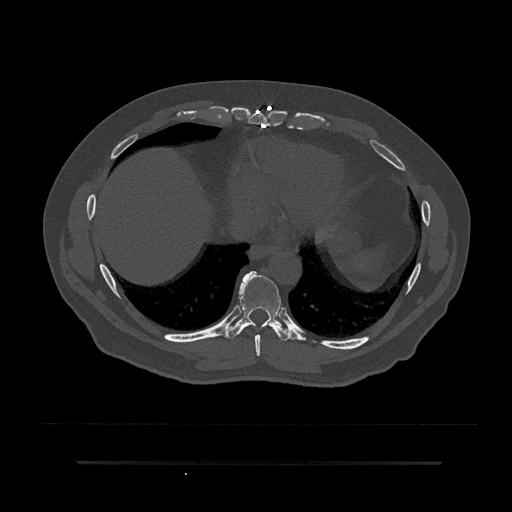
CT including the spine, one axial slice. Position 393 of 797 along the scan axis. Reconstruction kernel Br40s/3. 120 kVp. Bone window (W 1800 / L 400 HU). 0.5 mm slice thickness. 512 × 512 image matrix, field of view 464 × 464 mm. Male patient, age 59 years. Case-level facts recorded for this patient, not image findings: primary cancer: bile ducts; vertebrae with lytic lesions (as recorded): T10.
Structures marked on this image (semi-automatically segmented with operator editing):
- T8 vertebra: bounding box <255,334,261,356> (left, top, right, bottom; pixels)
- T9 vertebra: <227,271,290,341>